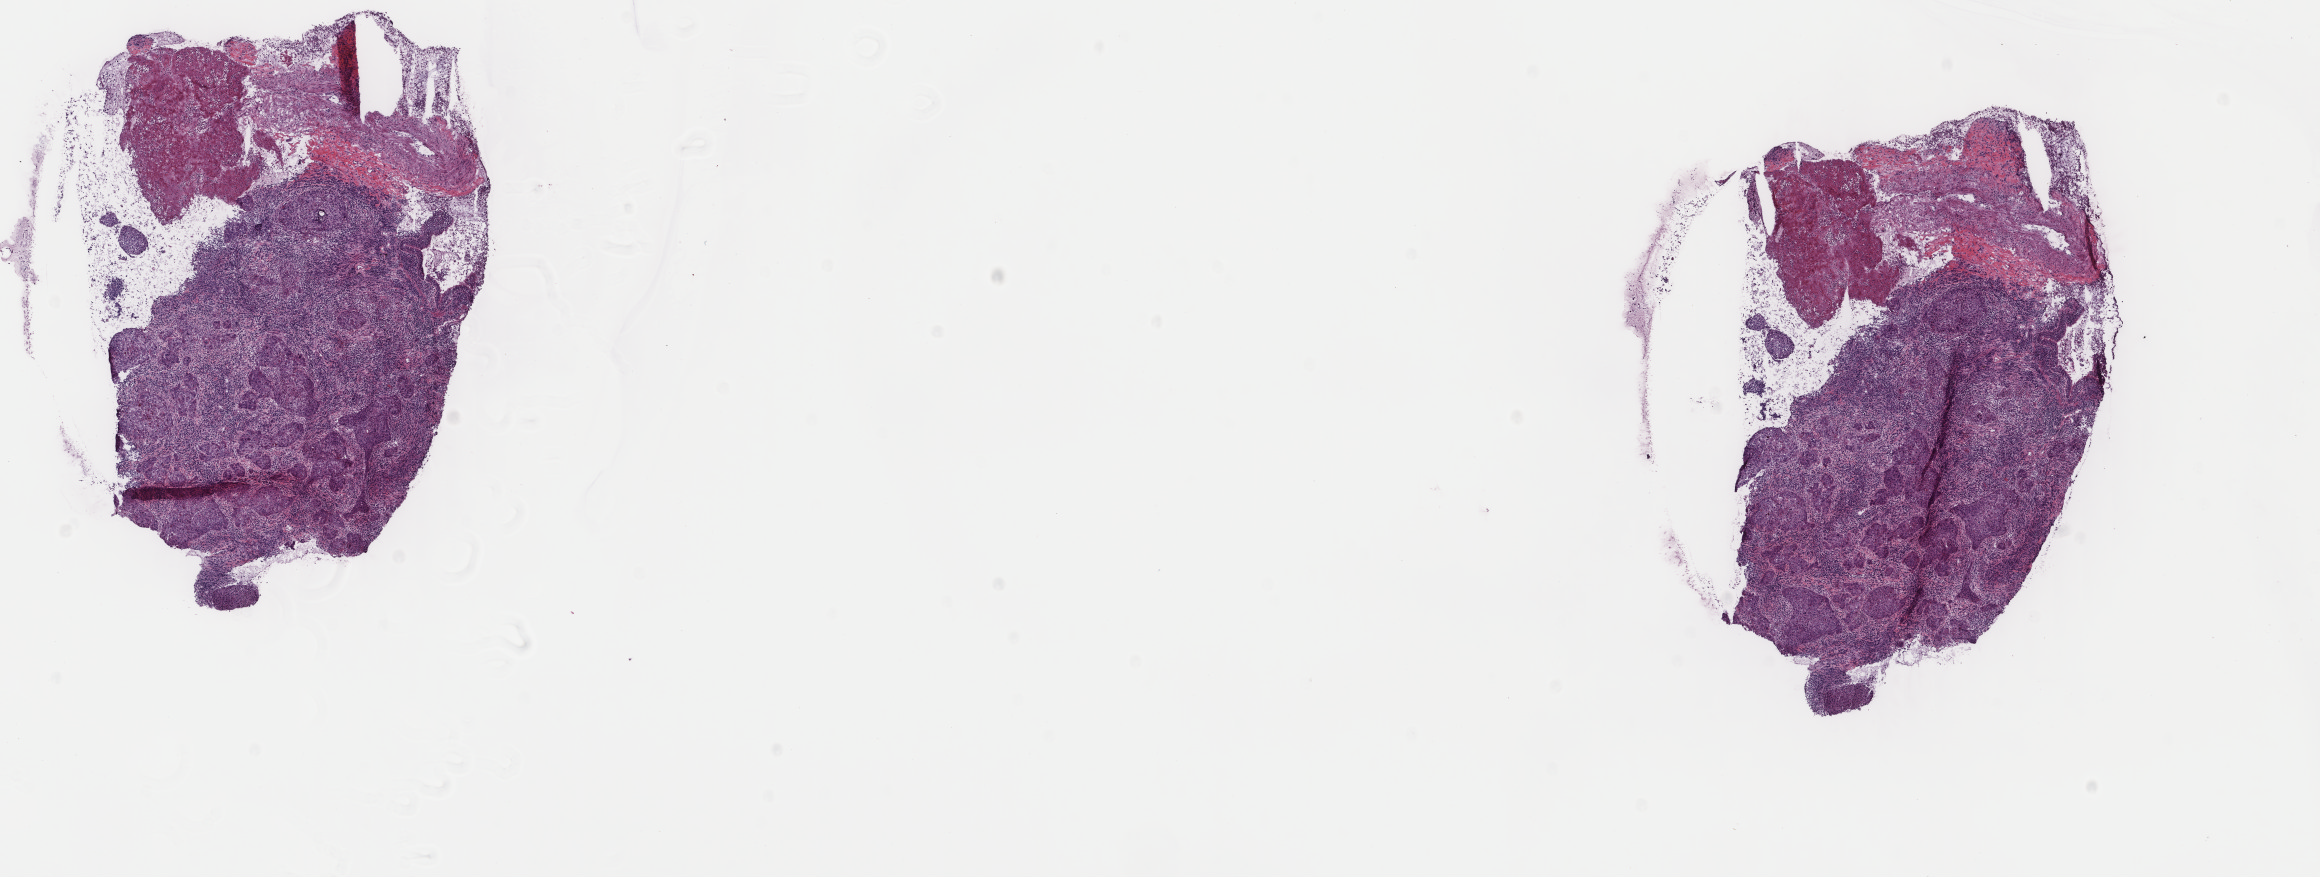
H&E whole-slide image, shown as a low-resolution overview of the whole scanned area (about 18.4 x 7.0 mm, acquisition: 40x scan); frozen section from the top of the tissue portion; sample: primary tumour, lung. Female, age 76 years at initial diagnosis. Pathologist review of this section (percent, as recorded): tumour cells 40%, tumour nuclei 70%, normal cells 10%, stromal cells 50%, necrosis 0%. Infiltration values recorded for this section: lymphocyte infiltration 8%, monocyte infiltration 4%, neutrophil infiltration 20%.
- histologic diagnosis: Squamous cell carcinoma, NOS (upper lobe, lung)
- AJCC pathologic stage: IA
- laterality: left